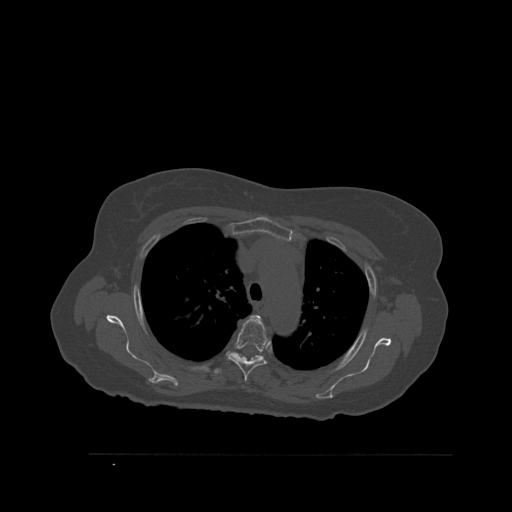
CT including the spine, one axial slice. Position 407 of 527 along the scan axis. Bone window (W 1800 / L 400 HU). 1.5 mm slice thickness. 512 × 512 image matrix, field of view 470 × 470 mm. Female patient, age 73 years. Case-level facts recorded for this patient, not image findings: primary cancer: breast; vertebrae with lytic lesions (as recorded): L2.
Structures marked on this image (semi-automatic segmentation, software-assisted and operator-edited):
- T3 vertebra: bounding box <251,316,261,319> (left, top, right, bottom; pixels)
- T4 vertebra: <229,316,267,383>
- T5 vertebra: <214,356,261,375>